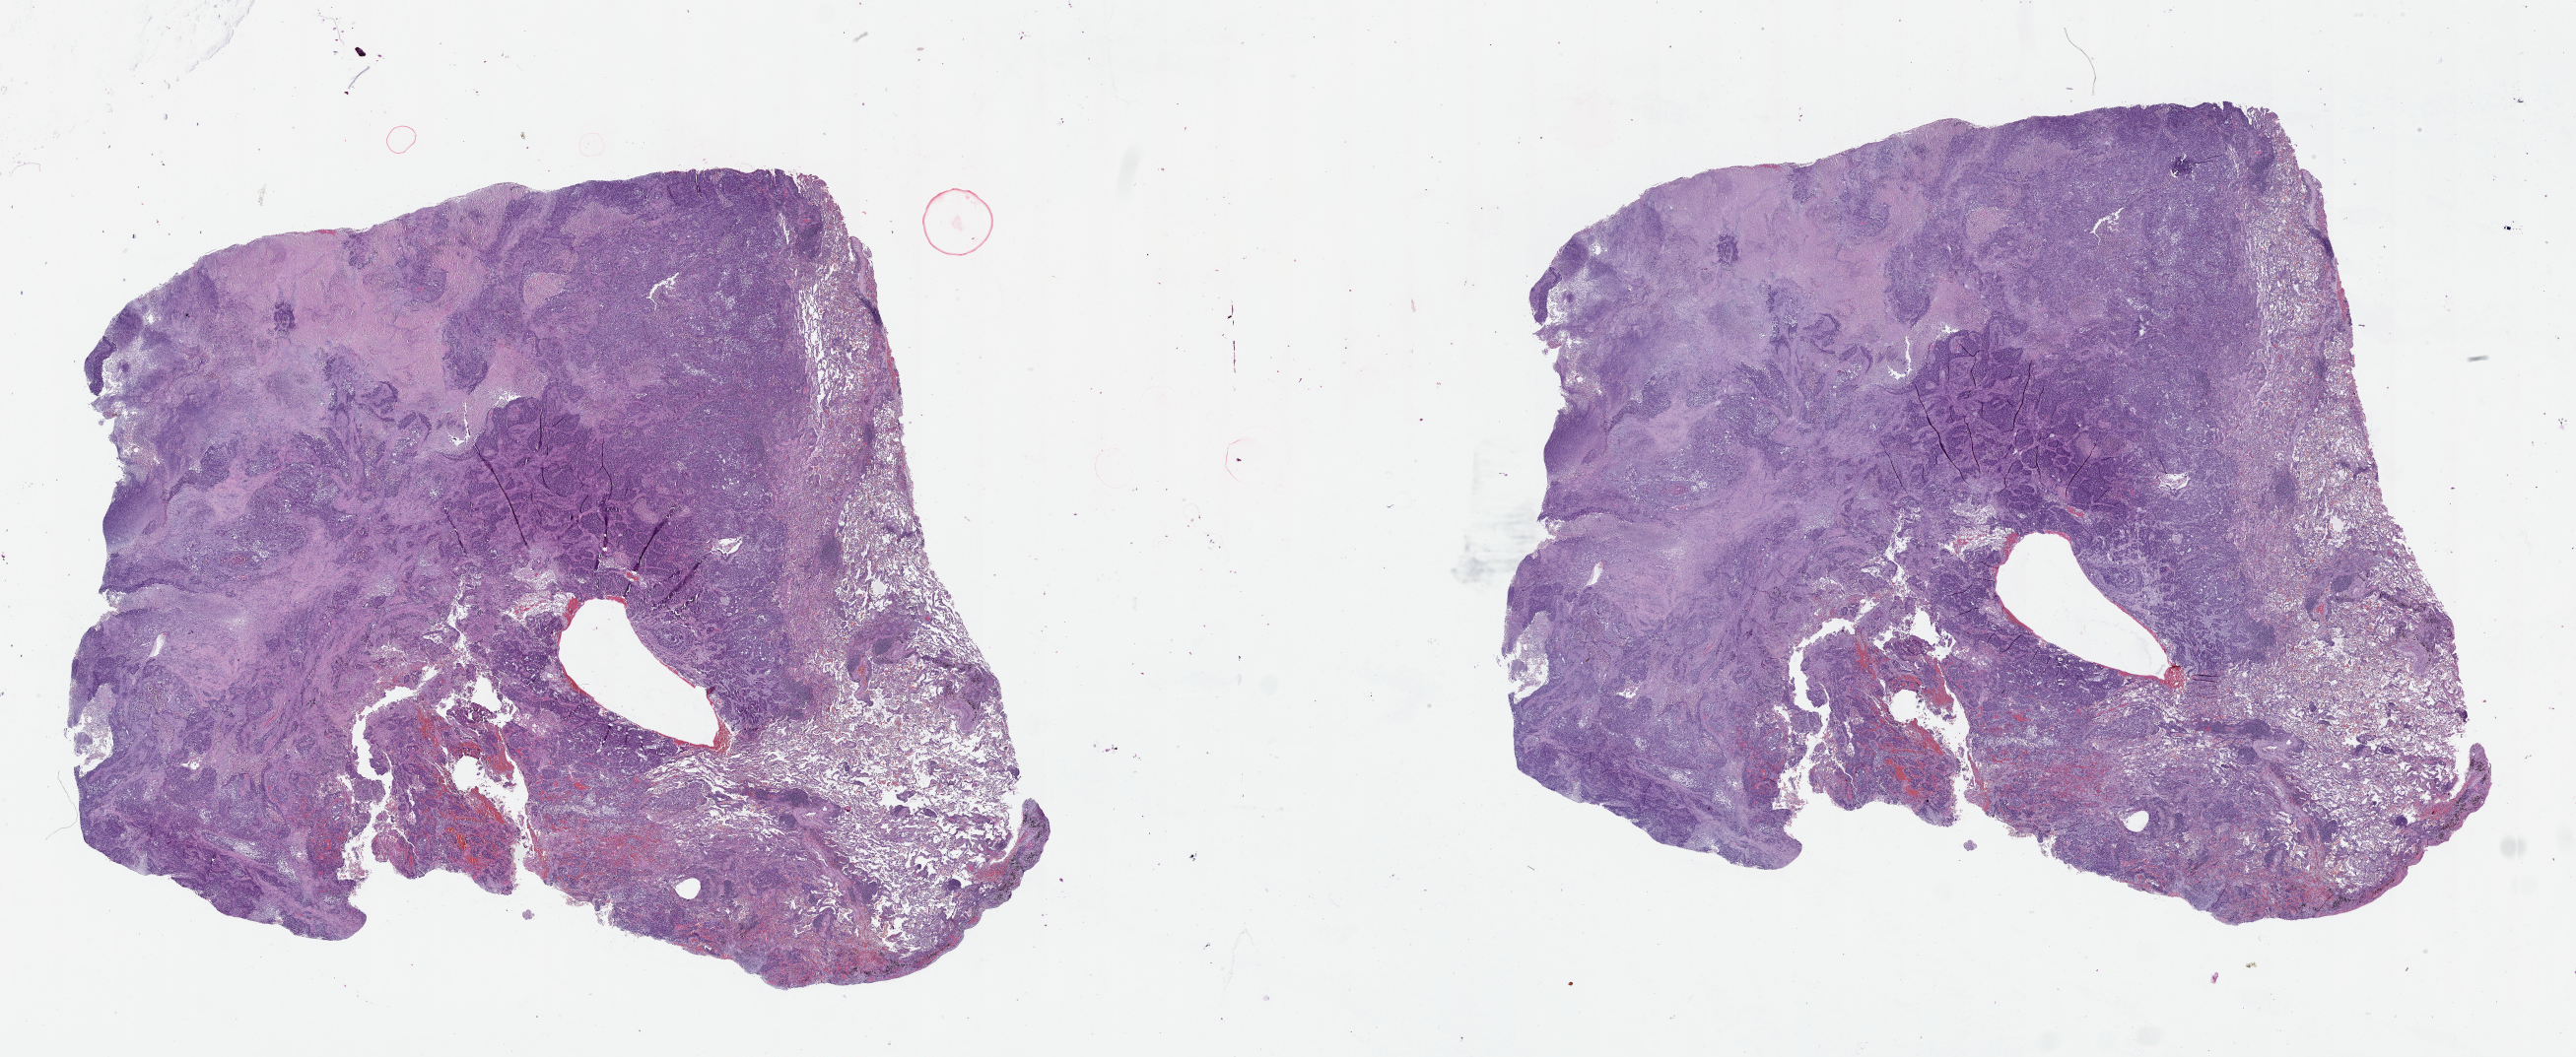
Digitized Hematoxylin and eosin (H&E) stained tissue section (whole slide) — a low-resolution overview of the entire scanned area, about 42.1 x 17.3 mm; lung, tissue type not recorded.
Patient diagnosis (cohort enrolment): squamous cell carcinoma (lung).